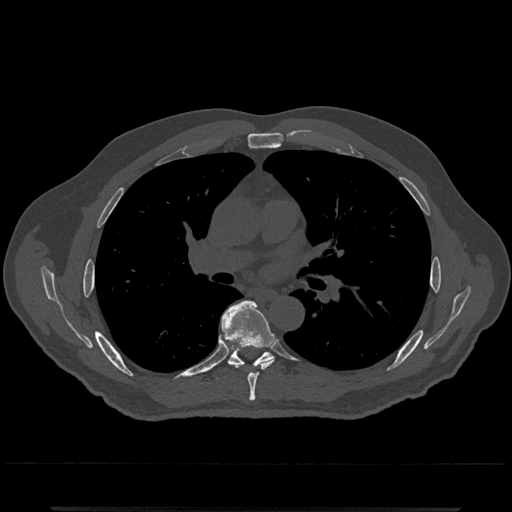
CT including the spine, one axial slice. Position 751 of 797 along the scan axis. Bone window (W 1800 / L 400 HU). 0.5 mm slice thickness. 512 × 512 image matrix, field of view 393 × 393 mm. Male patient, age 67 years. From the clinical record (not read from this slice): primary cancer: prostate.
Outlined on this slice (semi-automatic segmentation, software-assisted and operator-edited):
- T6 vertebra: bounding box [x1, y1, x2, y2] px = [221, 300, 275, 401]
- T7 vertebra: [214, 334, 273, 379]